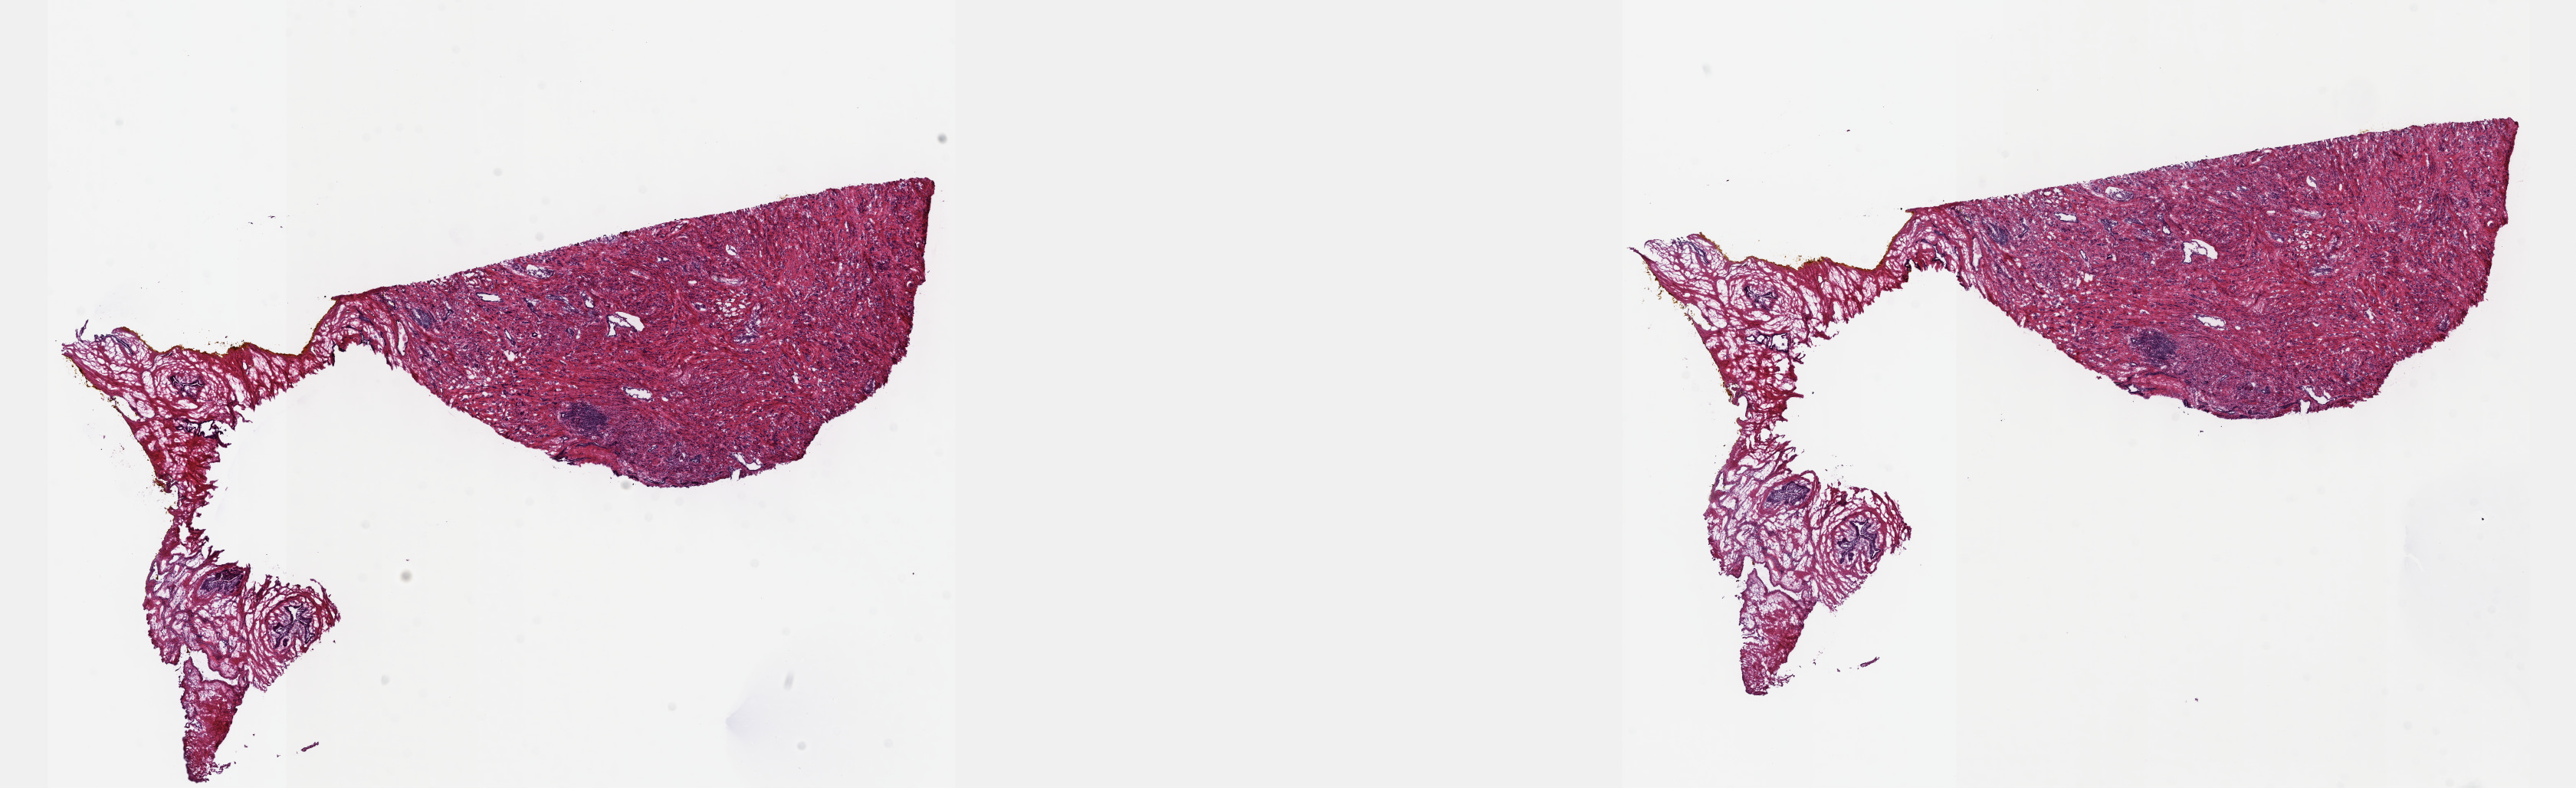
Digitized H&E-stained tissue section (whole slide) — whole scanned area (about 27.2 x 8.3 mm, from a 40x scan) shown as a low-resolution overview. Frozen section. Sample: primary tumour, prostate. Male, age 69 years at initial diagnosis. Gleason score: 9 (5+4). Slide review estimates, as recorded: tumour cells 60%, tumour nuclei 60%, normal cells 0%, stromal cells 40%, necrosis 0%. Inflammatory infiltration, as recorded: lymphocyte infiltration 40%, monocyte infiltration 20%, neutrophil infiltration 20%.
- lymph nodes positive (case pathology): 2 of 14 examined
- diagnosis: Adenocarcinoma, NOS (prostate gland)